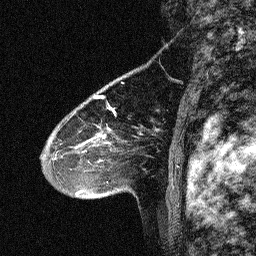
Breast MRI (dynamic contrast-enhanced), one sagittal slice. Slice 44 of 64 in the series (ordered by position). Dynamic contrast-enhanced study with each time point stored as its own series, time point 2 of 3 at this slice position (early post-contrast, ordered by acquisition time). 1.5 T. TE 4.5 ms, TR 11 ms. 2.06 mm slice thickness. 256 × 256 image matrix, field of view 200 × 200 mm. Patient: female, 46 years. From the clinical record (not read from this slice): setting: breast cancer imaged before/during neoadjuvant chemotherapy; receptor status: HER2-positive.
Annotated regions visible in this slice (semi-automatic segmentation, software-assisted and operator-edited):
- analysis volume of interest (the breast-tissue region the enhancement analysis was run in; not a lesion): bounding box <42,80,150,180> (left, top, right, bottom; pixels)
- tumour enhancement mask (voxels above the 90 % enhancement threshold inside the analysis volume of interest): <61,97,112,152>